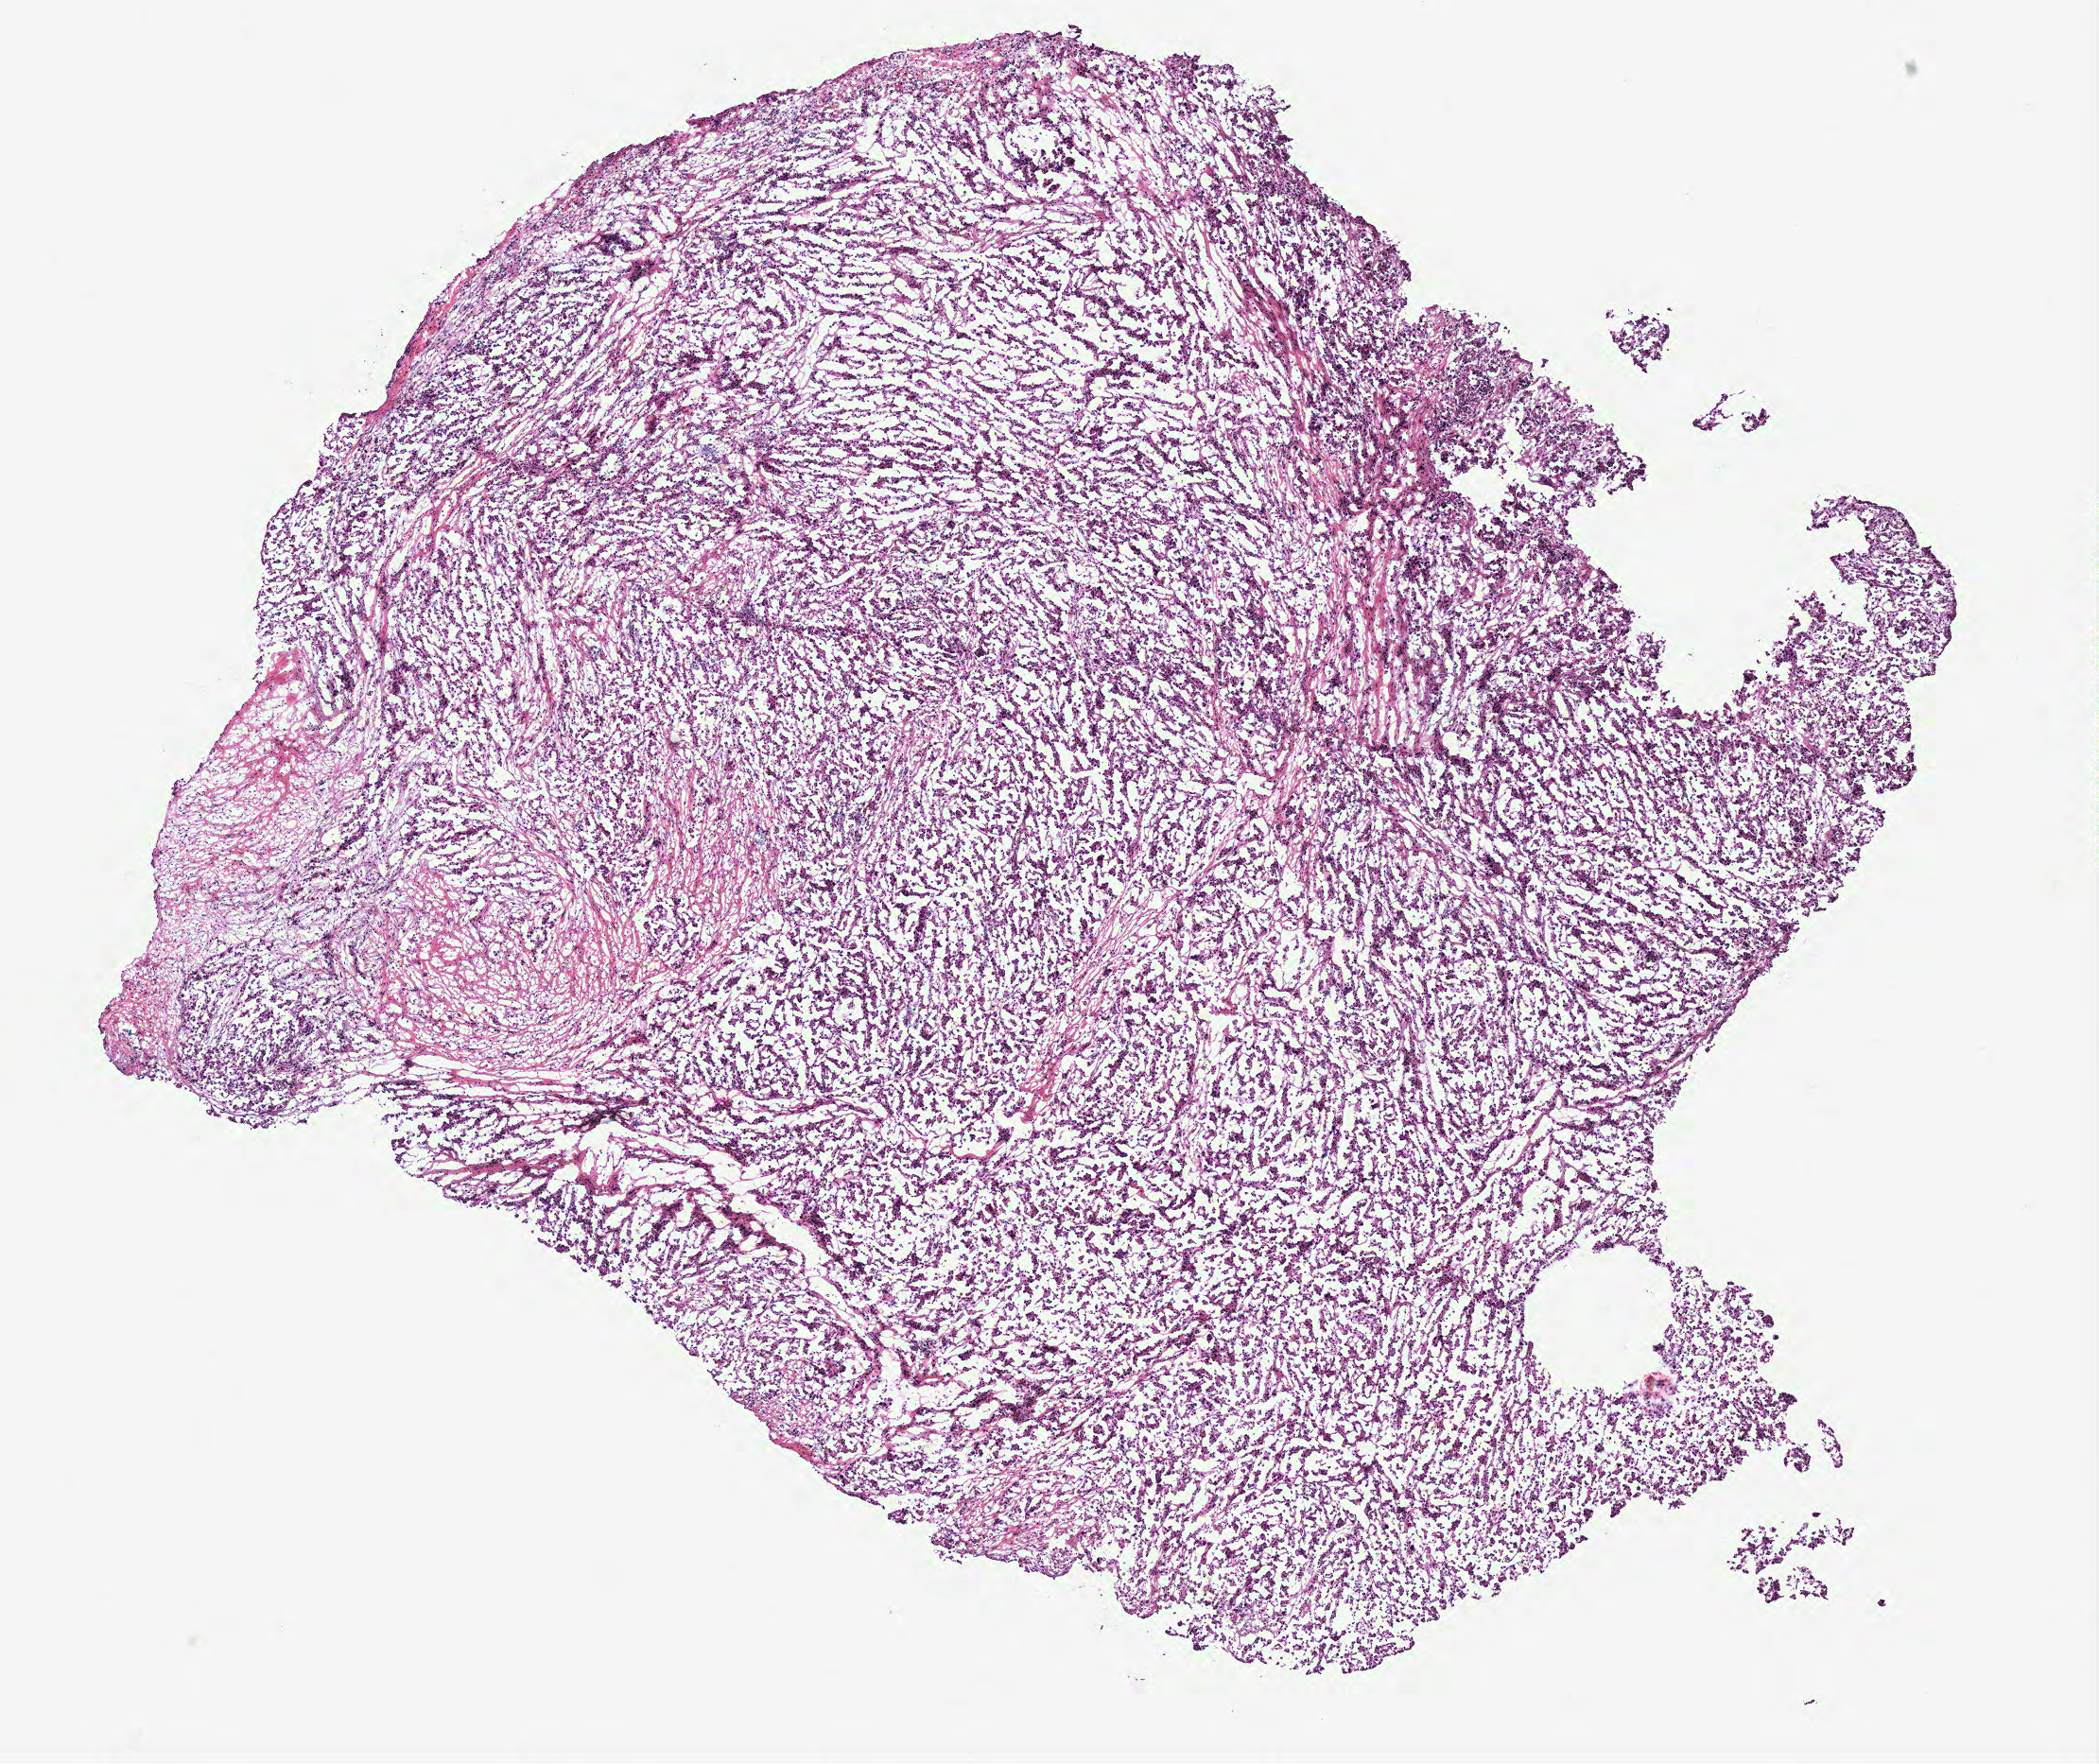
Digitized H&E tissue section (whole slide) — a low-resolution overview of the entire scanned area, about 8.9 x 7.5 mm, ovary, tumour tissue. Female, 57 y/o.
* diagnosis: Serous adenocarcinoma, NOS
* primary tumour site (as recorded): ovary